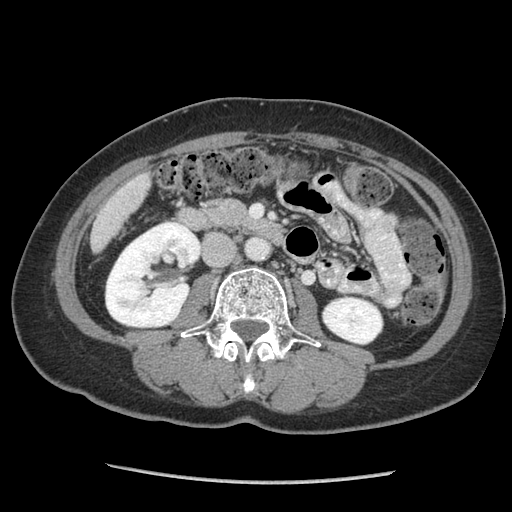
Contrast-enhanced abdominal CT (liver protocol), one axial slice. Slice 18 of 105 in the series (ordered by position). Reconstruction kernel STANDARD. Soft-tissue window (W 400 / L 40 HU). 512 × 512 image matrix, field of view 340 × 340 mm. Case-level facts recorded for this patient, not image findings: diagnosis: hepatocellular carcinoma (patient treated with transarterial chemoembolisation; whether this scan precedes or follows treatment is not stated here); TNM stage (as recorded): Stage-I; Child-Pugh class: A; tumour differentiation: moderately differentiated; tumour nodularity: uninodular.
Outlined on this slice (semi-automatic segmentation, software-assisted and operator-edited):
- liver parenchyma outside the tumour (the mass and vessels are separate outlines, so this box may not span the whole liver): bounding box (x1, y1, x2, y2) in pixels: (90, 172, 150, 251)